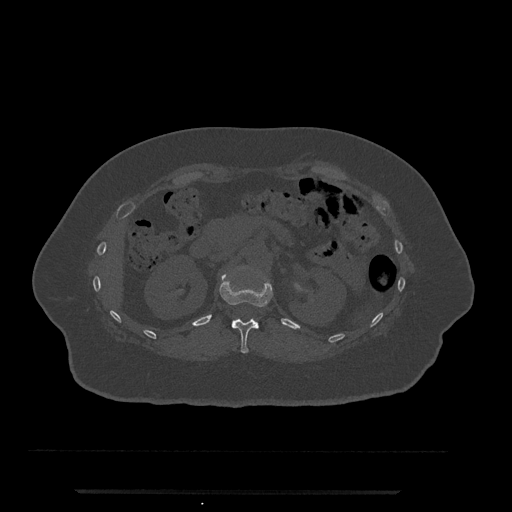
CT including the spine, one axial slice. Slice 153 of 797 in the series (ordered by position). Reconstruction kernel Br40s/3. 120 kVp. Bone window (W 1800 / L 400 HU). 0.5 mm slice thickness. 512 × 512 image matrix, field of view 440 × 440 mm. Patient: female, 51 years. Case-level facts recorded for this patient, not image findings: primary cancer: neuro; vertebrae with lytic lesions (as recorded): T8.
Annotated regions visible in this slice (semi-automatic segmentation, software-assisted and operator-edited):
- T12 vertebra: bounding box (x1, y1, x2, y2) in pixels: (219, 274, 273, 354)